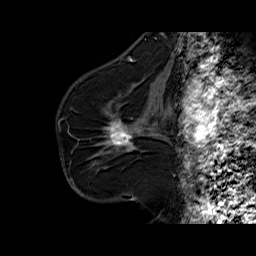
Breast MRI (dynamic contrast-enhanced), one sagittal slice; position 37 of 60 along the scan axis; dynamic contrast-enhanced series, time point 2 of 6 at this slice position (early post-contrast); 1.5 T; TE 6.3 ms, TR 32.5 ms; 256 × 256 image matrix. Female patient. Case-level facts recorded for this patient, not image findings: setting: breast cancer imaged before/during neoadjuvant chemotherapy; receptor status: HR-positive, HER2-negative.
Outlined on this slice (semi-automatic segmentation, software-assisted and operator-edited):
- analysis volume of interest (the breast-tissue region the enhancement analysis was run in; not a lesion): bounding box <94,103,161,164> (left, top, right, bottom; pixels)
- tumour enhancement mask (voxels above the 100 % enhancement threshold inside the analysis volume of interest): <109,120,132,145>